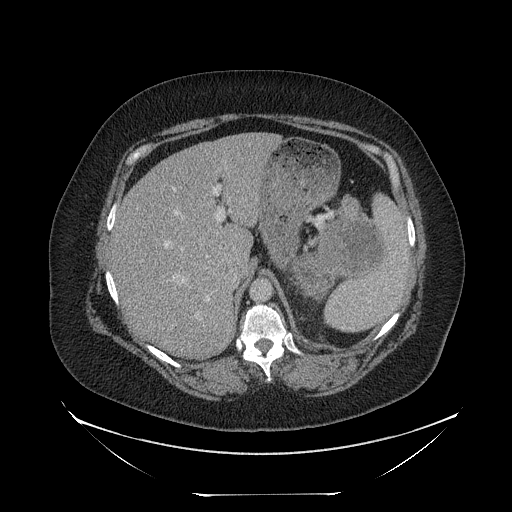
Contrast-enhanced abdominal CT, one axial slice. Position 164 of 205 along the scan axis. 120 kVp. Intravenous contrast given. Soft-tissue window (W 400 / L 40 HU). 2.5 mm slice thickness. 512 × 512 image matrix, field of view 500 × 500 mm. Patient: female, 53 years. Case-level facts recorded for this patient, not image findings: diagnosis: adrenocortical carcinoma; tumour side: left adrenal; tumour size at pathology: 17 cm; Ki-67 index: 20 %; stage (as recorded): 3.
Structures marked on this image (semi-automatically segmented with operator editing):
- mass: bounding box (x1, y1, x2, y2) in pixels: (293, 223, 381, 298)